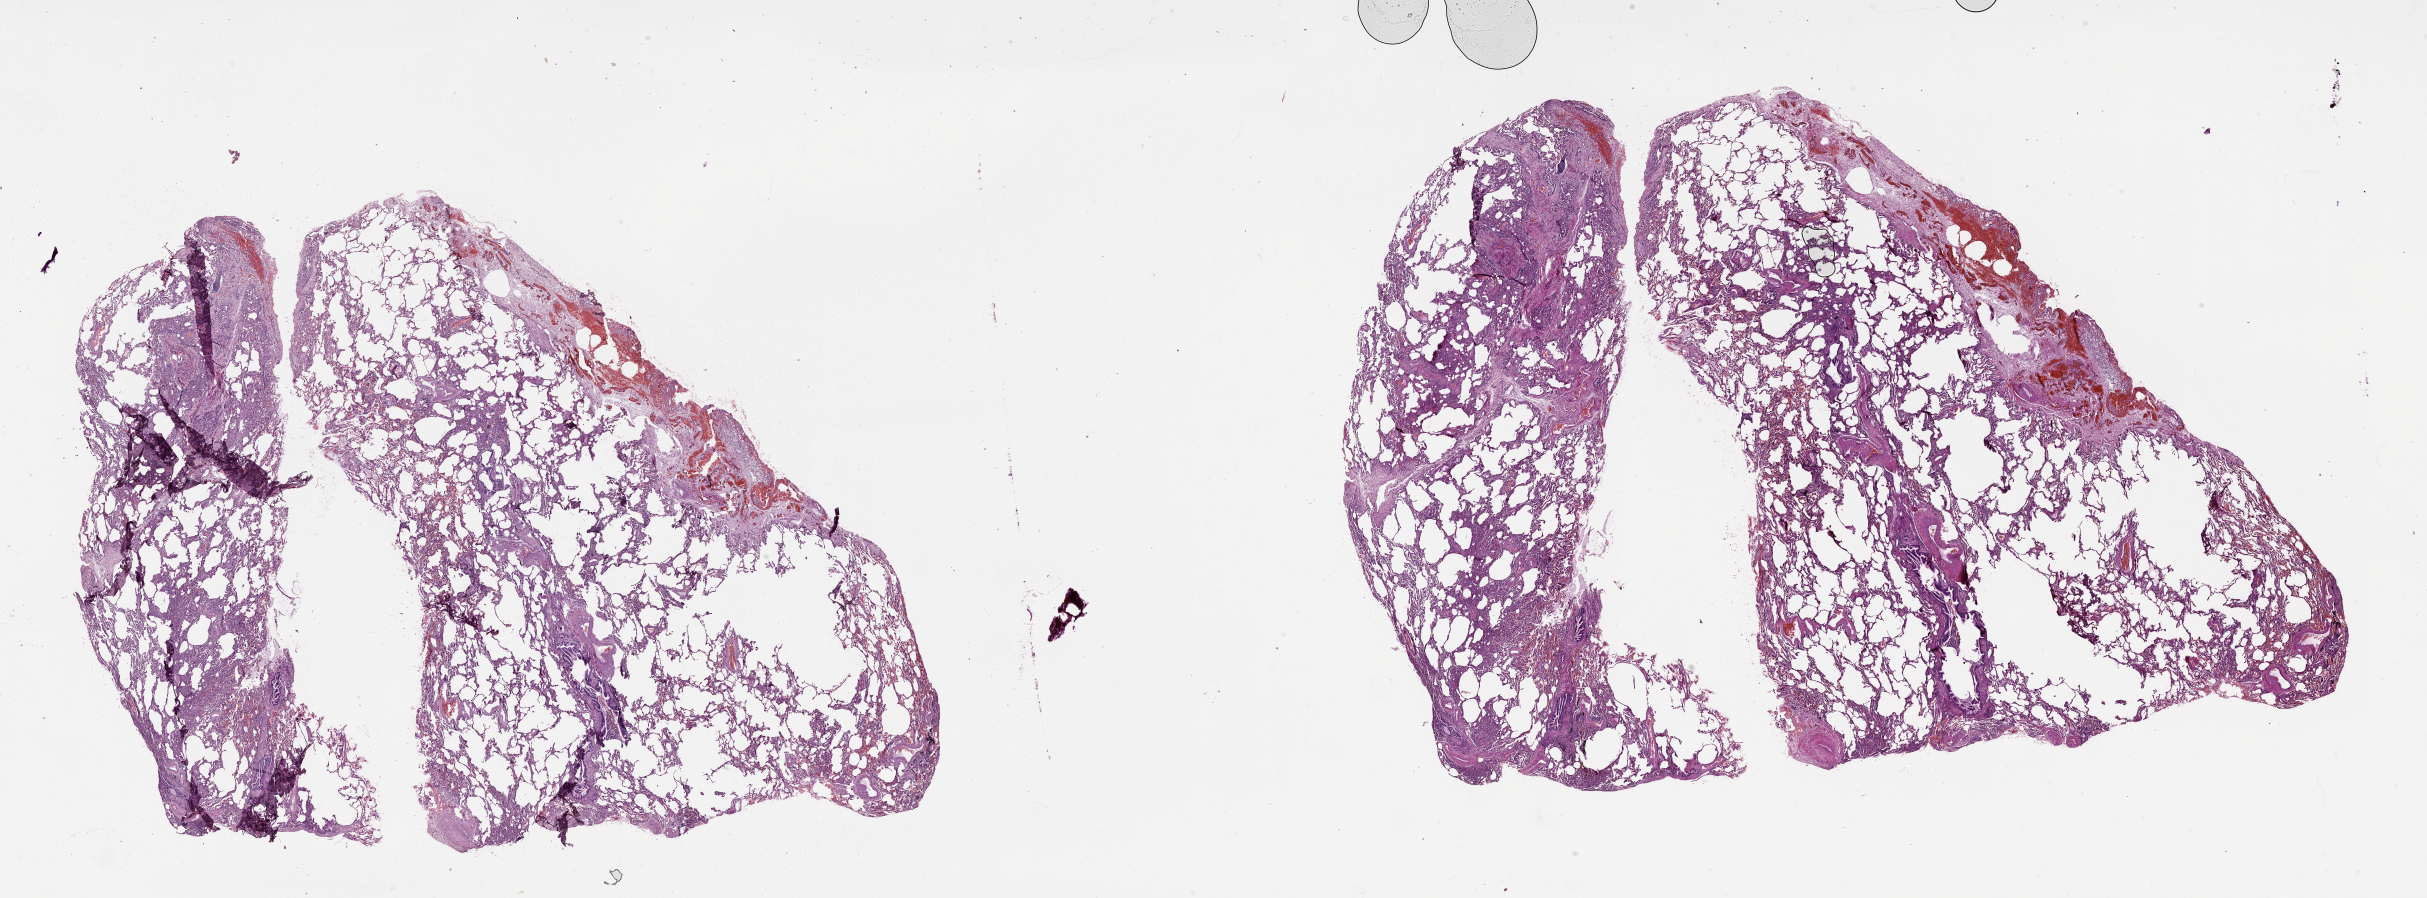
Digitized Hematoxylin and eosin (H&E) stained tissue section (whole slide), low-resolution overview of the scanned area, about 39.1 x 14.5 mm, lung, normal (non-tumour) tissue. 53-year-old male patient.
• this section: normal (non-tumour) tissue from the same patient
• patient diagnosis (cohort enrolment): squamous cell carcinoma (lung)